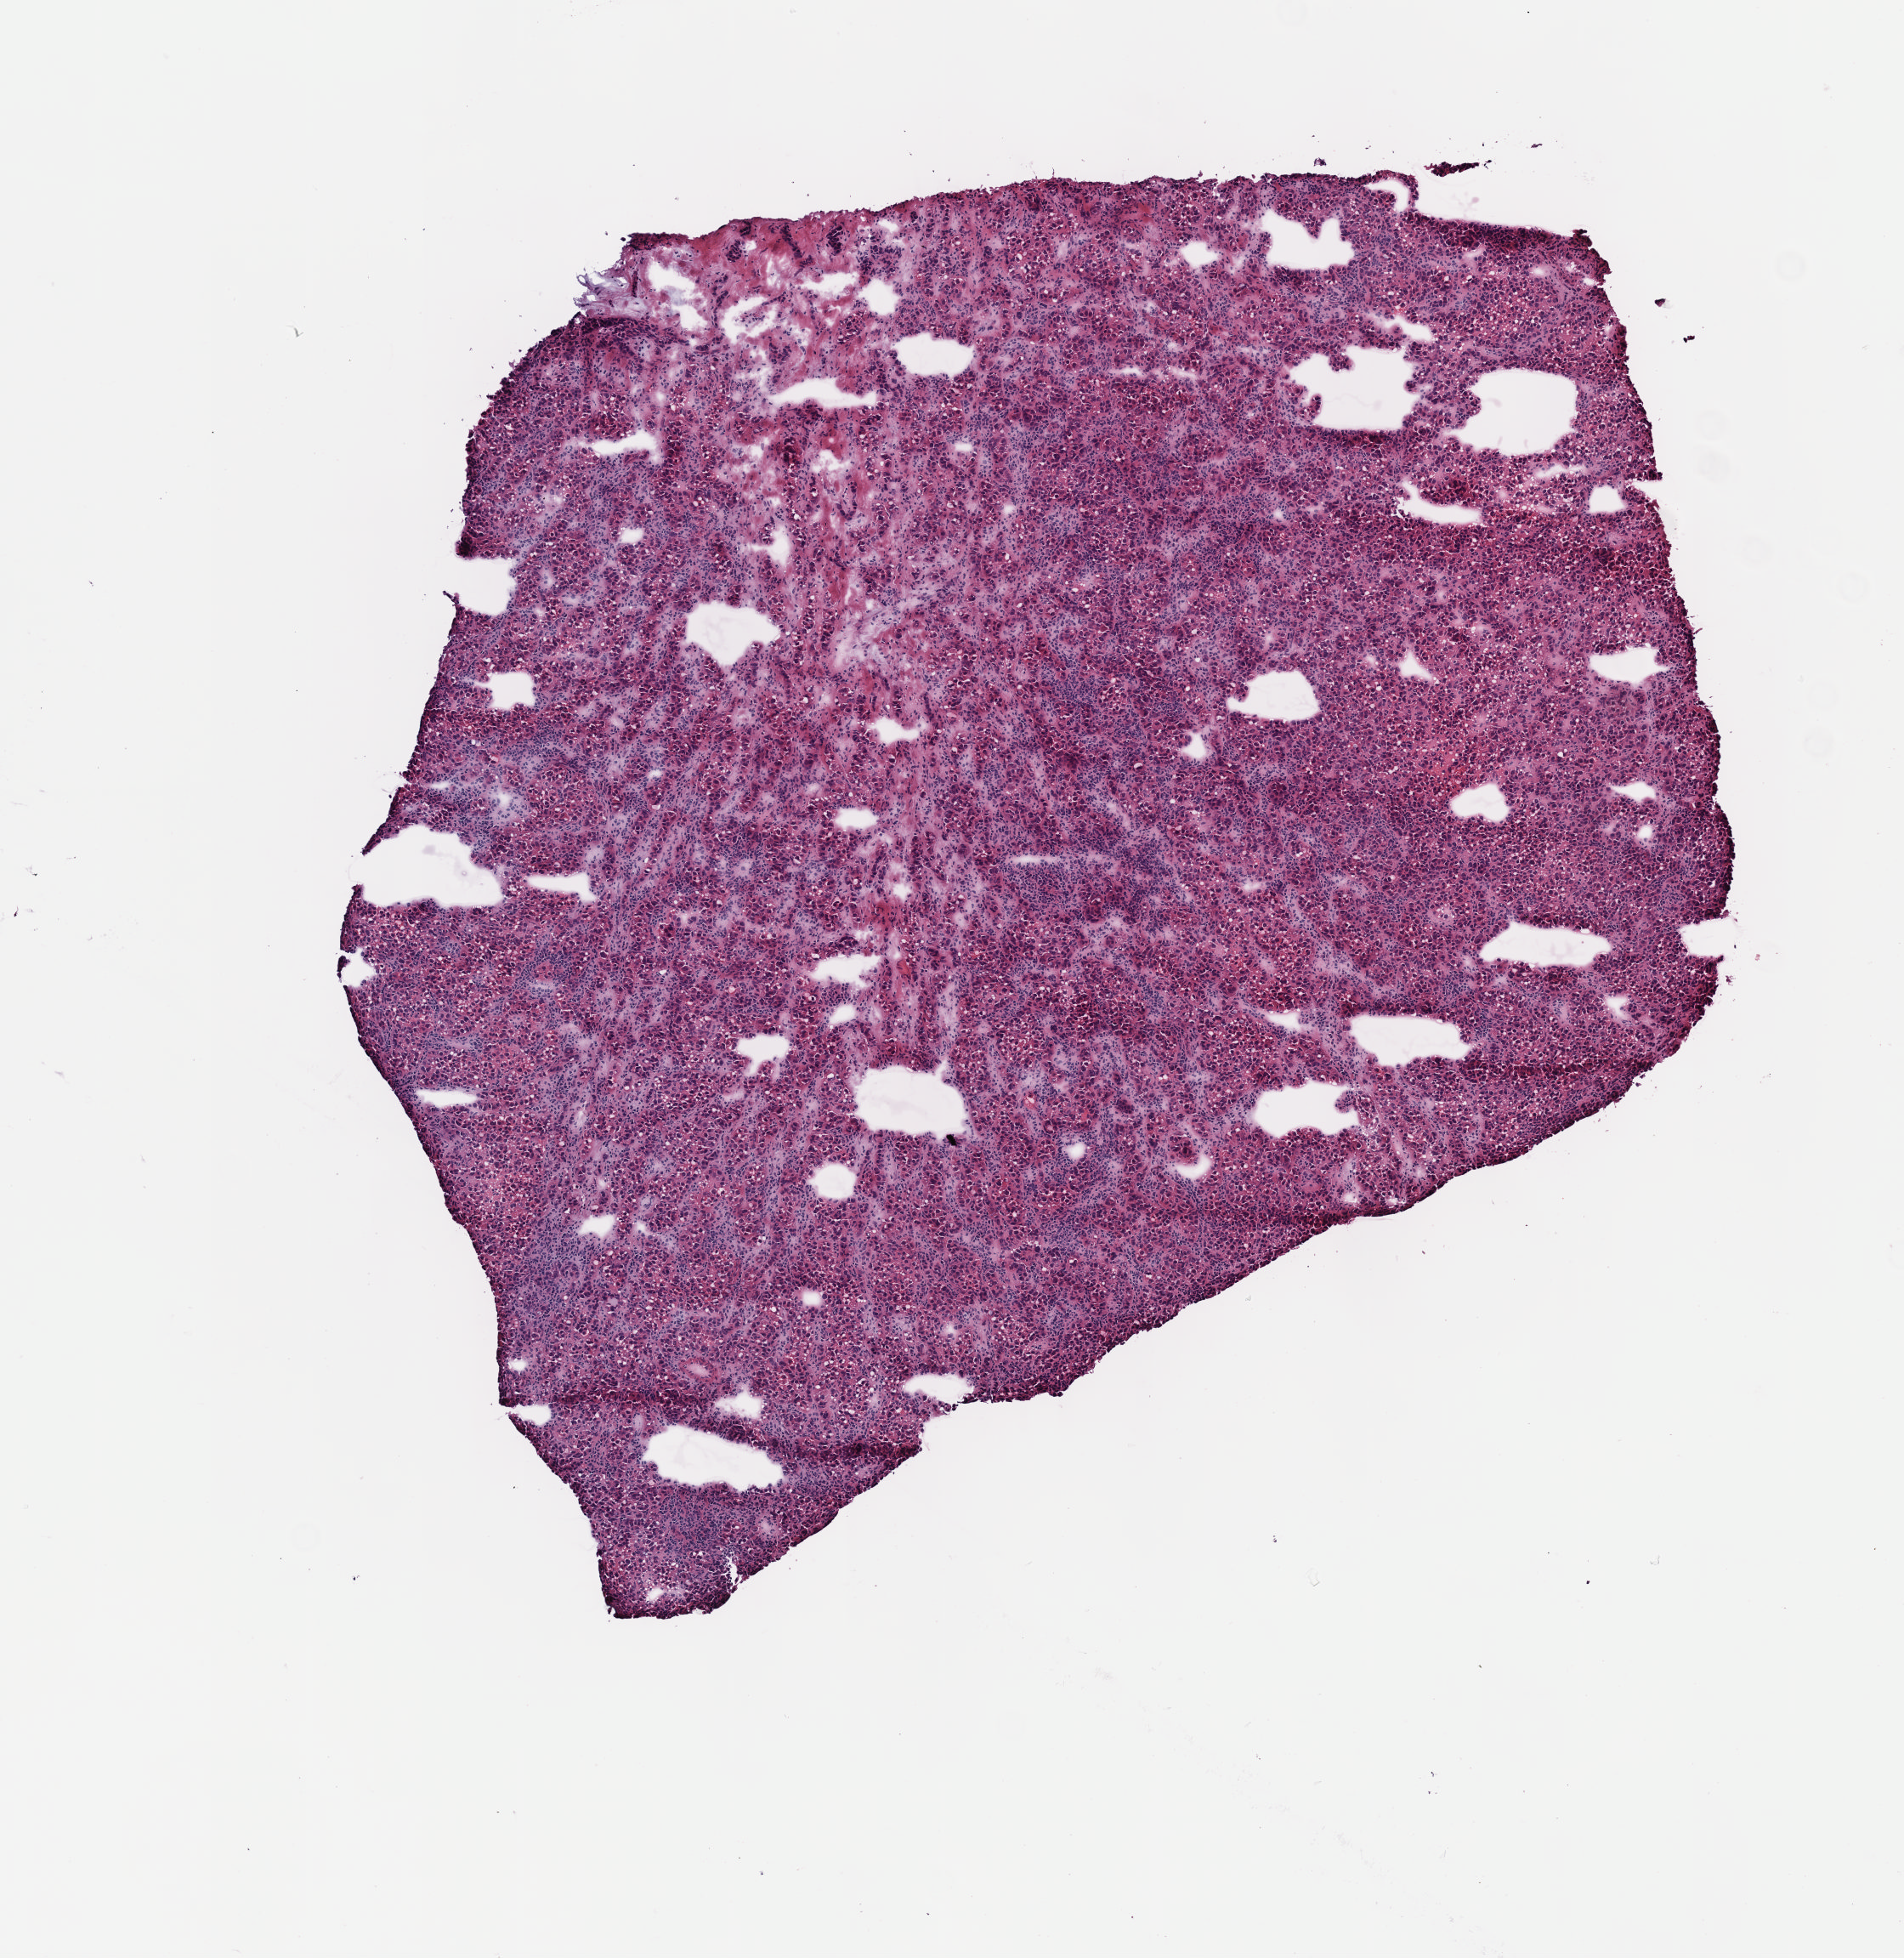
H&E whole-slide image — a low-resolution overview of the entire scanned area, about 4.5 x 4.7 mm (acquisition: 40x scan); frozen section from the top of the tissue portion; liver, primary tumour sample. Patient: female, age at initial diagnosis 43 years. Histologic grade: G3 (poorly differentiated). Slide review estimates, as recorded: tumour cells 90%, tumour nuclei 95%, normal cells 0%, stromal cells 10%, necrosis 0%. Inflammatory infiltration, as recorded: lymphocyte infiltration 0%, monocyte infiltration 0%, neutrophil infiltration 0%.
AJCC pathologic stage: I (7th edition). Pathologic diagnosis: Hepatocellular carcinoma, NOS.